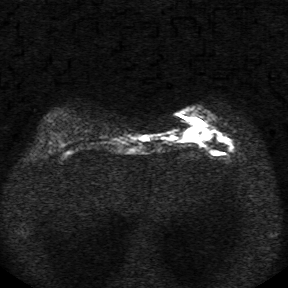
Breast MRI, one axial slice. Position 9 of 34 along the scan axis. Diffusion-weighted series; image 2 of 4 stored at this slice position (different b-values; order by instance number). 1.5 T. 288 × 288 image matrix. Female patient.
Annotated regions visible in this slice (expert manual segmentation):
- tumour on diffusion-weighted imaging: bounding box <183,118,210,141> (left, top, right, bottom; pixels)